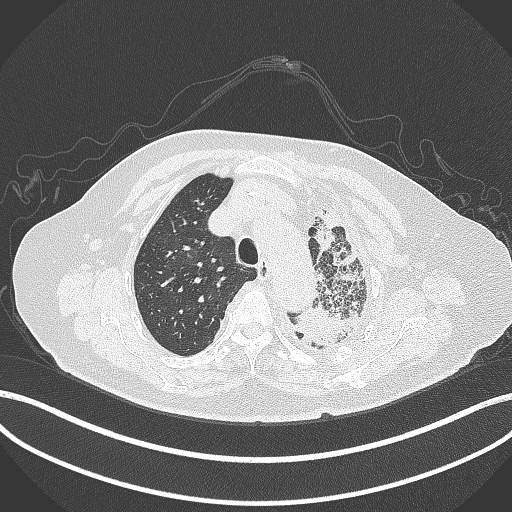
Chest CT, one axial slice. Position 306 of 399 along the scan axis. Lung window (W 1500 / L -600 HU). 1 mm slice thickness. 512 × 512 image matrix, field of view 400 × 400 mm. Patient: female, 75 years. From the clinical record (not read from this slice): clinical TNM (as recorded): T3 N3 M1.
Annotated regions visible in this slice (rectangle marked by the reading radiologist):
- lung tumour (recorded histology: adenocarcinoma): box from (x=288, y=297) to (x=366, y=353) px